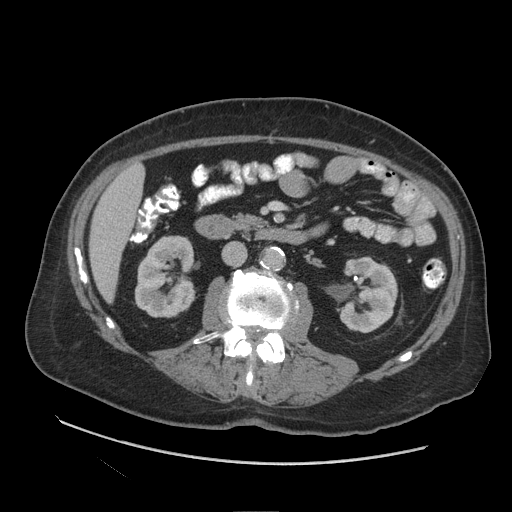
Contrast-enhanced abdominal CT (liver protocol), one axial slice; slice 30 of 109 in the series (ordered by position); 140 kVp; soft-tissue window (W 400 / L 40 HU); 512 × 512 image matrix. From the clinical record (not read from this slice): diagnosis: hepatocellular carcinoma (patient treated with transarterial chemoembolisation; whether this scan precedes or follows treatment is not stated here); TNM stage (as recorded): Stage-I; Child-Pugh class: A.
Outlined on this slice (semi-automatic segmentation, software-assisted and operator-edited):
- liver parenchyma outside the tumour (the mass and vessels are separate outlines, so this box may not span the whole liver): bounding box (x1, y1, x2, y2) in pixels: (88, 164, 144, 302)